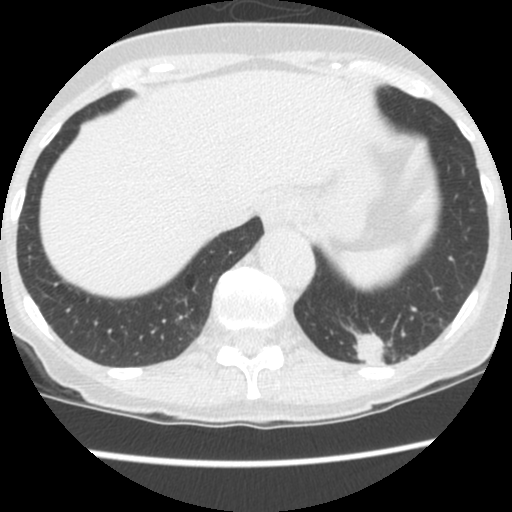
Low-dose screening chest CT, one axial slice. Slice 27 of 130 in the series (ordered by position). Lung window (W 1500 / L -600 HU). 2.5 mm slice thickness. 512 × 512 image matrix, field of view 290 × 290 mm.
Structures marked on this image (manually delineated by an expert):
- lesion 1 (tumor, lower lobe of left lung): bounding box [x1, y1, x2, y2] px = [354, 328, 392, 367]